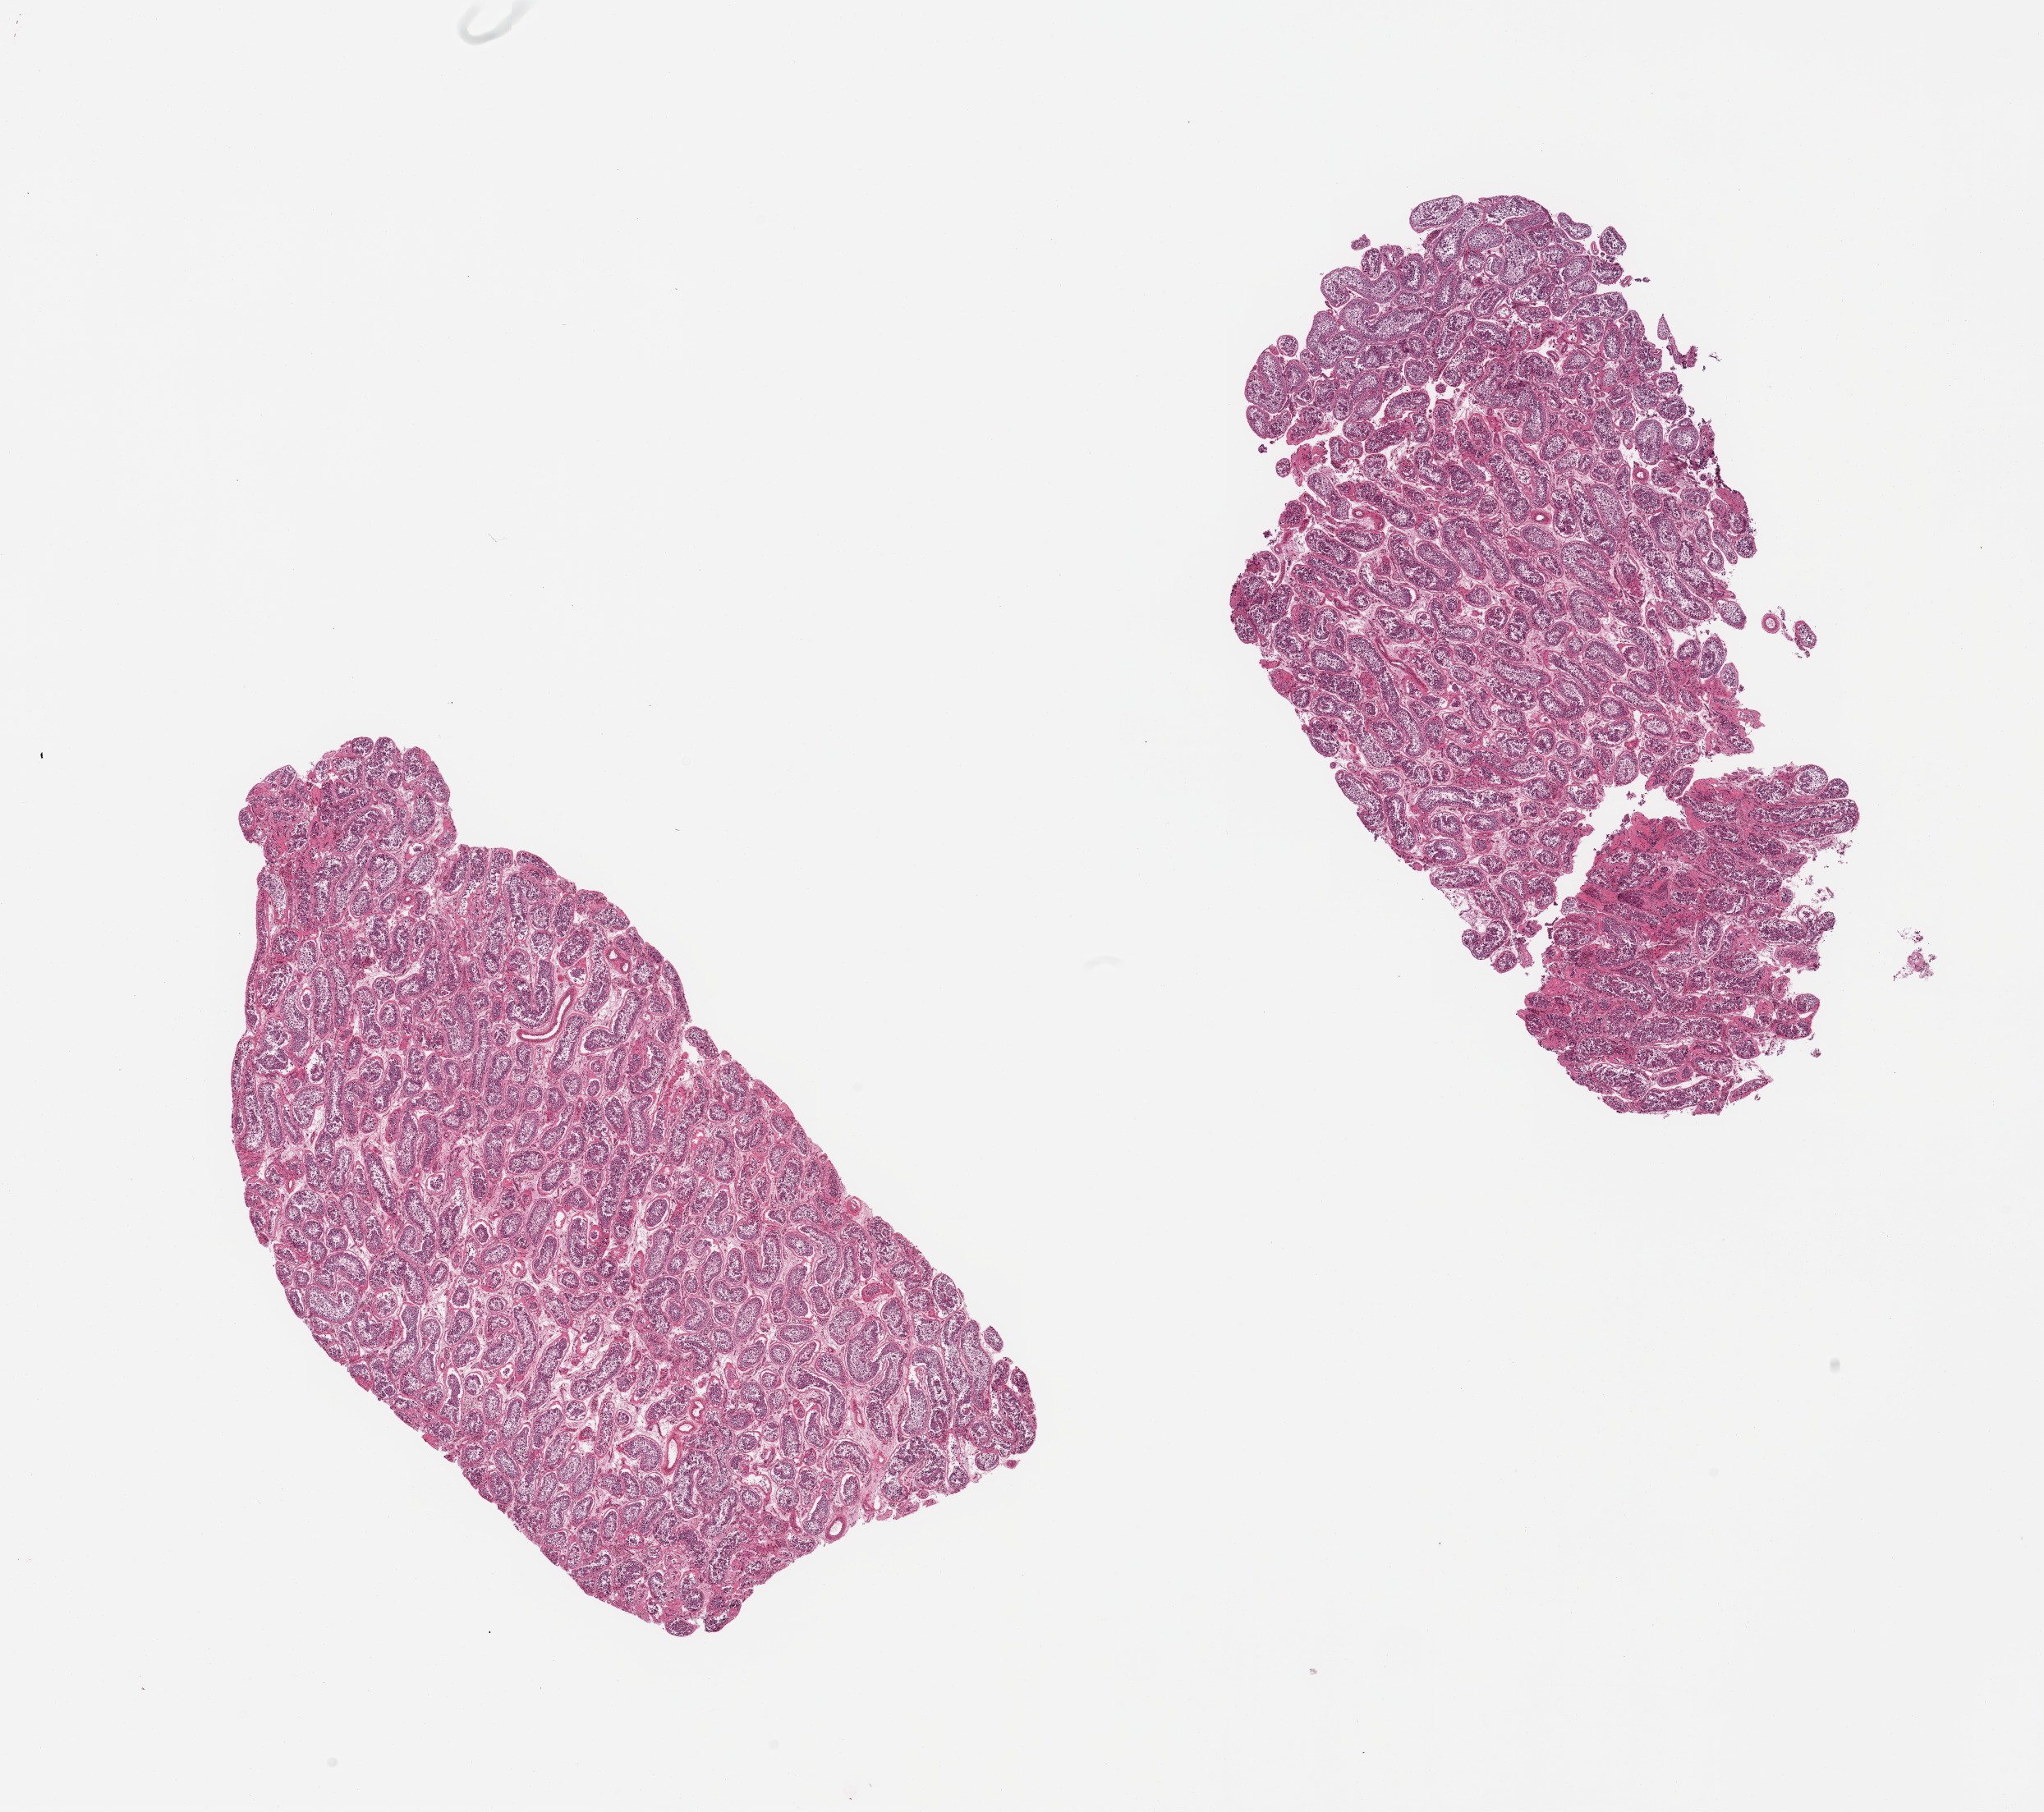
Digitized haematoxylin and eosin-stained section, a low-resolution overview of the entire scanned area, about 19.7 x 17.5 mm (acquisition: 20x scan); PAXgene-fixed, paraffin-embedded tissue; target tissue: testis; donor tissue sample. Donor: male.
• reviewer comment on this tissue sample: 2 pieces; spermatogenesis observed